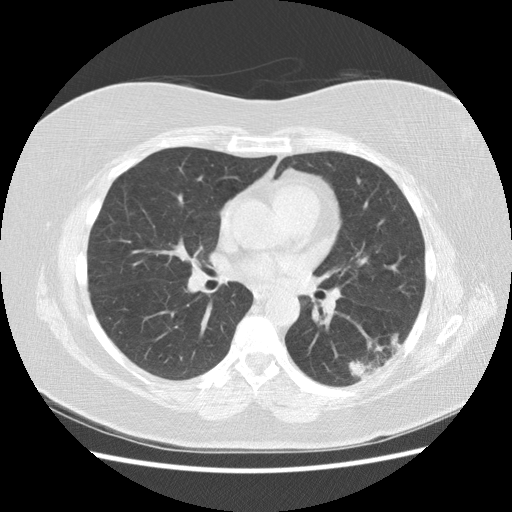
Low-dose screening chest CT, one axial slice; position 81 of 151 along the scan axis; lung window (W 1500 / L -600 HU); 2.5 mm slice thickness; 512 × 512 image matrix, field of view 360 × 360 mm.
Annotated regions visible in this slice (expert manual segmentation):
- lesion 1 (tumor, lower lobe of left lung): bounding box <349,332,403,381> (left, top, right, bottom; pixels)